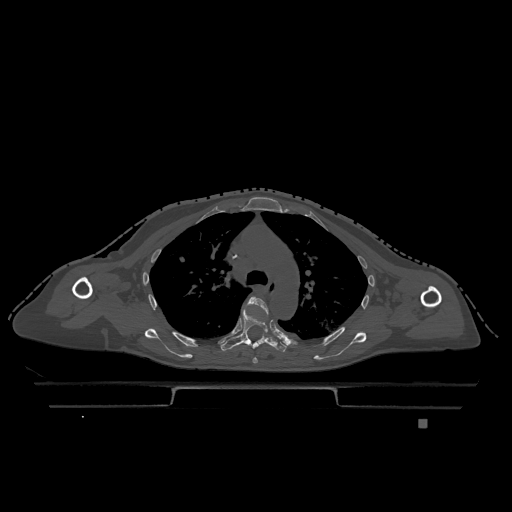
CT including the spine, one axial slice. Position 851 of 1317 along the scan axis. Bone window (W 1800 / L 400 HU). 0.5 mm slice thickness. 512 × 512 image matrix. Female patient, age 74 years. Case-level facts recorded for this patient, not image findings: primary cancer: lung.
Outlined on this slice (semi-automatically segmented with operator editing):
- T4 vertebra: bounding box <246,297,269,364> (left, top, right, bottom; pixels)
- T5 vertebra: <220,305,287,353>